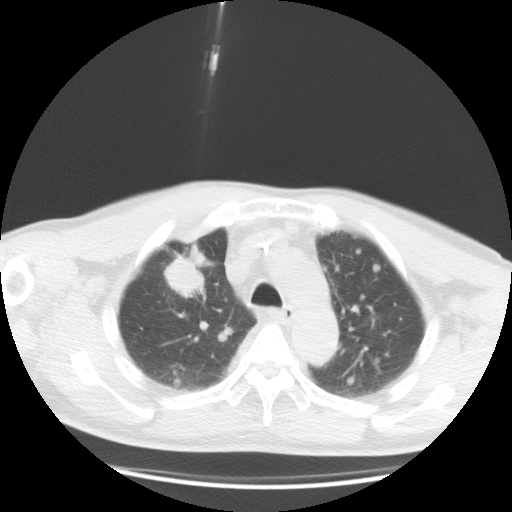
Chest CT, one axial slice; slice 22 of 35 in the series (ordered by position); reconstruction kernel STANDARD; 120 kVp; lung window (W 1500 / L -600 HU); 5 mm slice thickness; 512 × 512 image matrix, field of view 369 × 369 mm. Patient: male, 57 years. From the clinical record (not read from this slice): clinical TNM (as recorded): T2 N3 M1a.
Outlined on this slice (bounding box drawn by a radiologist):
- lung tumour (recorded histology: adenocarcinoma): bounding box [x1, y1, x2, y2] px = [160, 251, 208, 303]